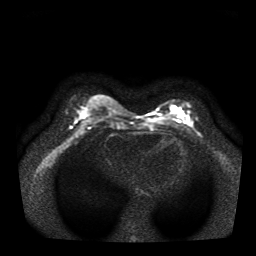
Breast MRI, one axial slice. Position 13 of 35 along the scan axis. Diffusion-weighted series; image 2 of 4 stored at this slice position (different b-values; order by instance number). 1.5 T. 5 mm slice thickness. 256 × 256 image matrix, field of view 330 × 330 mm. Female patient.
Outlined on this slice (outlined manually by an expert reader):
- tumour on diffusion-weighted imaging: bounding box [x1, y1, x2, y2] px = [172, 107, 180, 114]